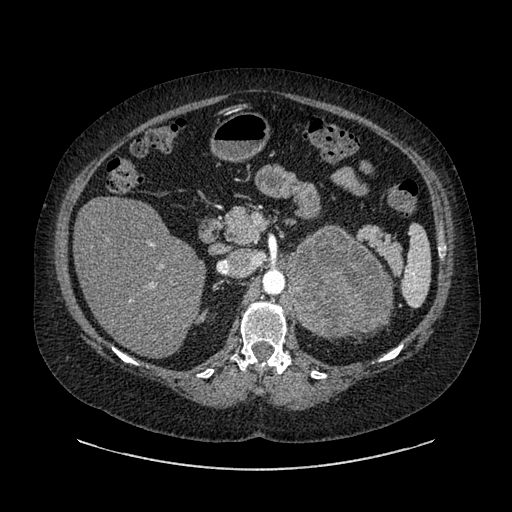
Contrast-enhanced abdominal CT, one axial slice. Position 558 of 769 along the scan axis. Reconstruction kernel SOFT. 120 kVp. Intravenous contrast given. Soft-tissue window (W 400 / L 40 HU). 0.62 mm slice thickness. 512 × 512 image matrix, field of view 460 × 460 mm. Female patient, age 61 years. From the clinical record (not read from this slice): diagnosis: adrenocortical carcinoma; tumour side: left adrenal; tumour size at pathology: 13 cm.
Annotated regions visible in this slice (semi-automatically segmented with operator editing):
- mass: bounding box <288,229,390,338> (left, top, right, bottom; pixels)